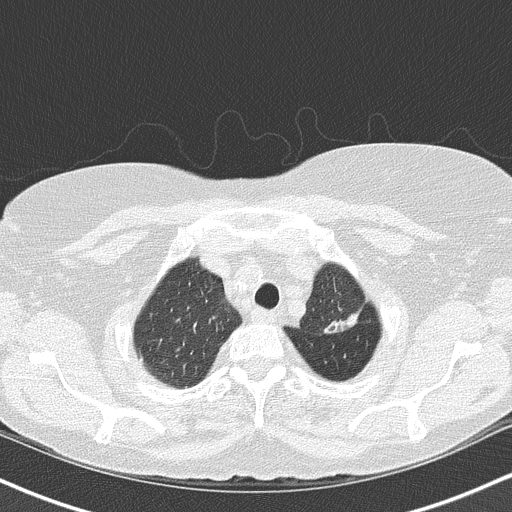
Low-dose screening chest CT, one axial slice; slice 129 of 147 in the series (ordered by position); lung window (W 1500 / L -600 HU); 2 mm slice thickness; 512 × 512 image matrix, field of view 320 × 320 mm.
Structures marked on this image (manually delineated by an expert):
- lesion 1 (tumor, upper lobe of left lung): bounding box (x1, y1, x2, y2) in pixels: (325, 314, 356, 333)